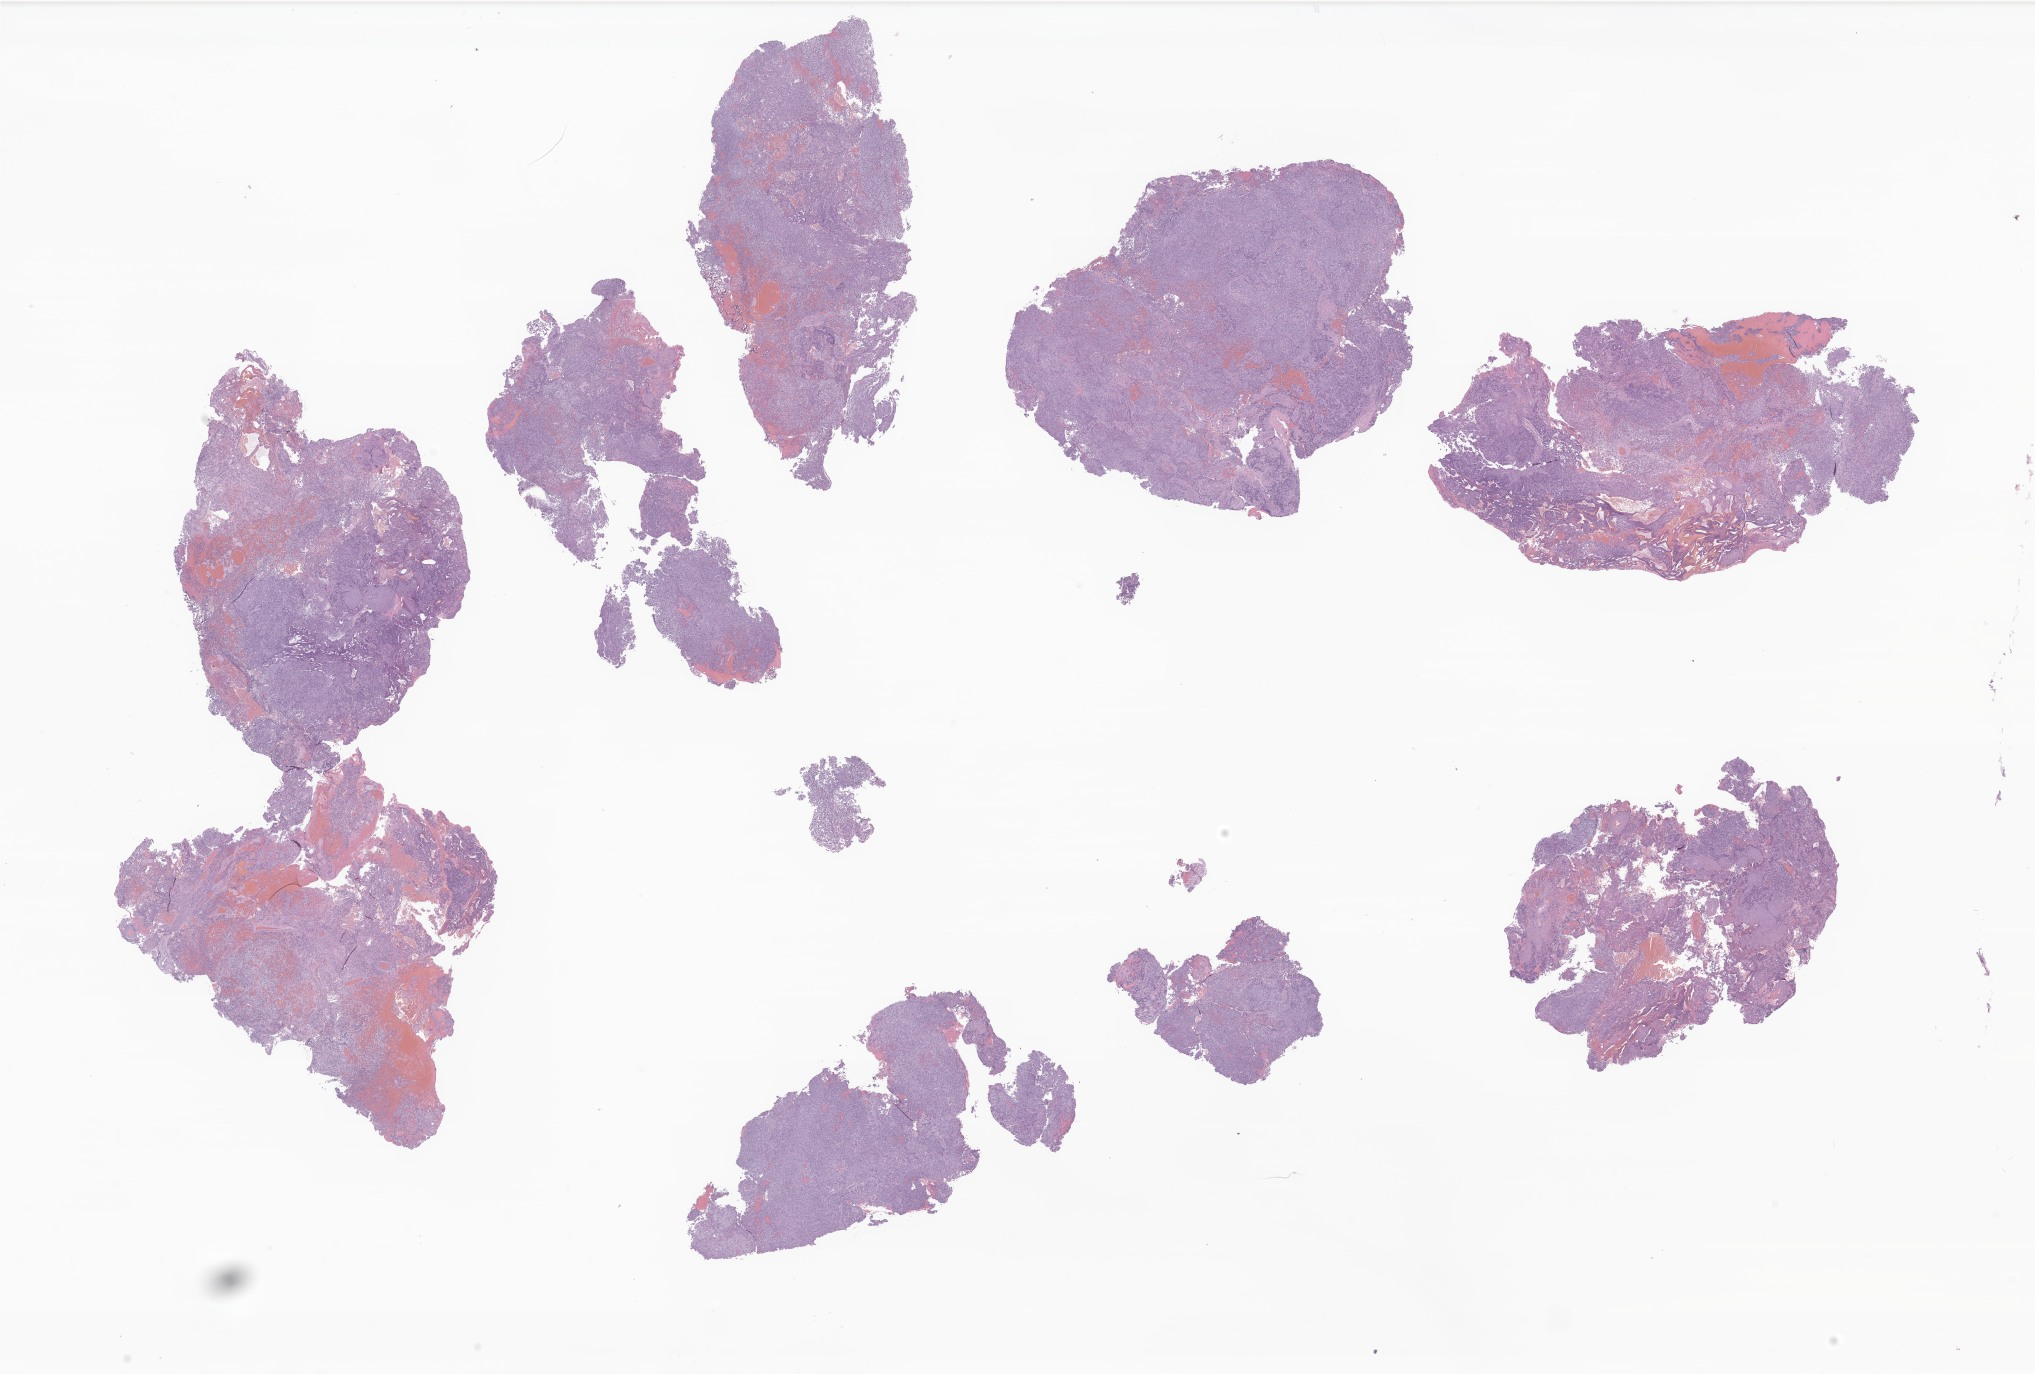
Haematoxylin and eosin whole-slide image of tumor tissue from the brain, whole scanned area (about 34.3 x 23.2 mm) shown as a low-resolution overview, FFPE section. Patient: male, age 768 days (about 2.1 years).
Diagnosis (ICD-O-3 morphology term): Atypical teratoid/rhabdoid tumor.